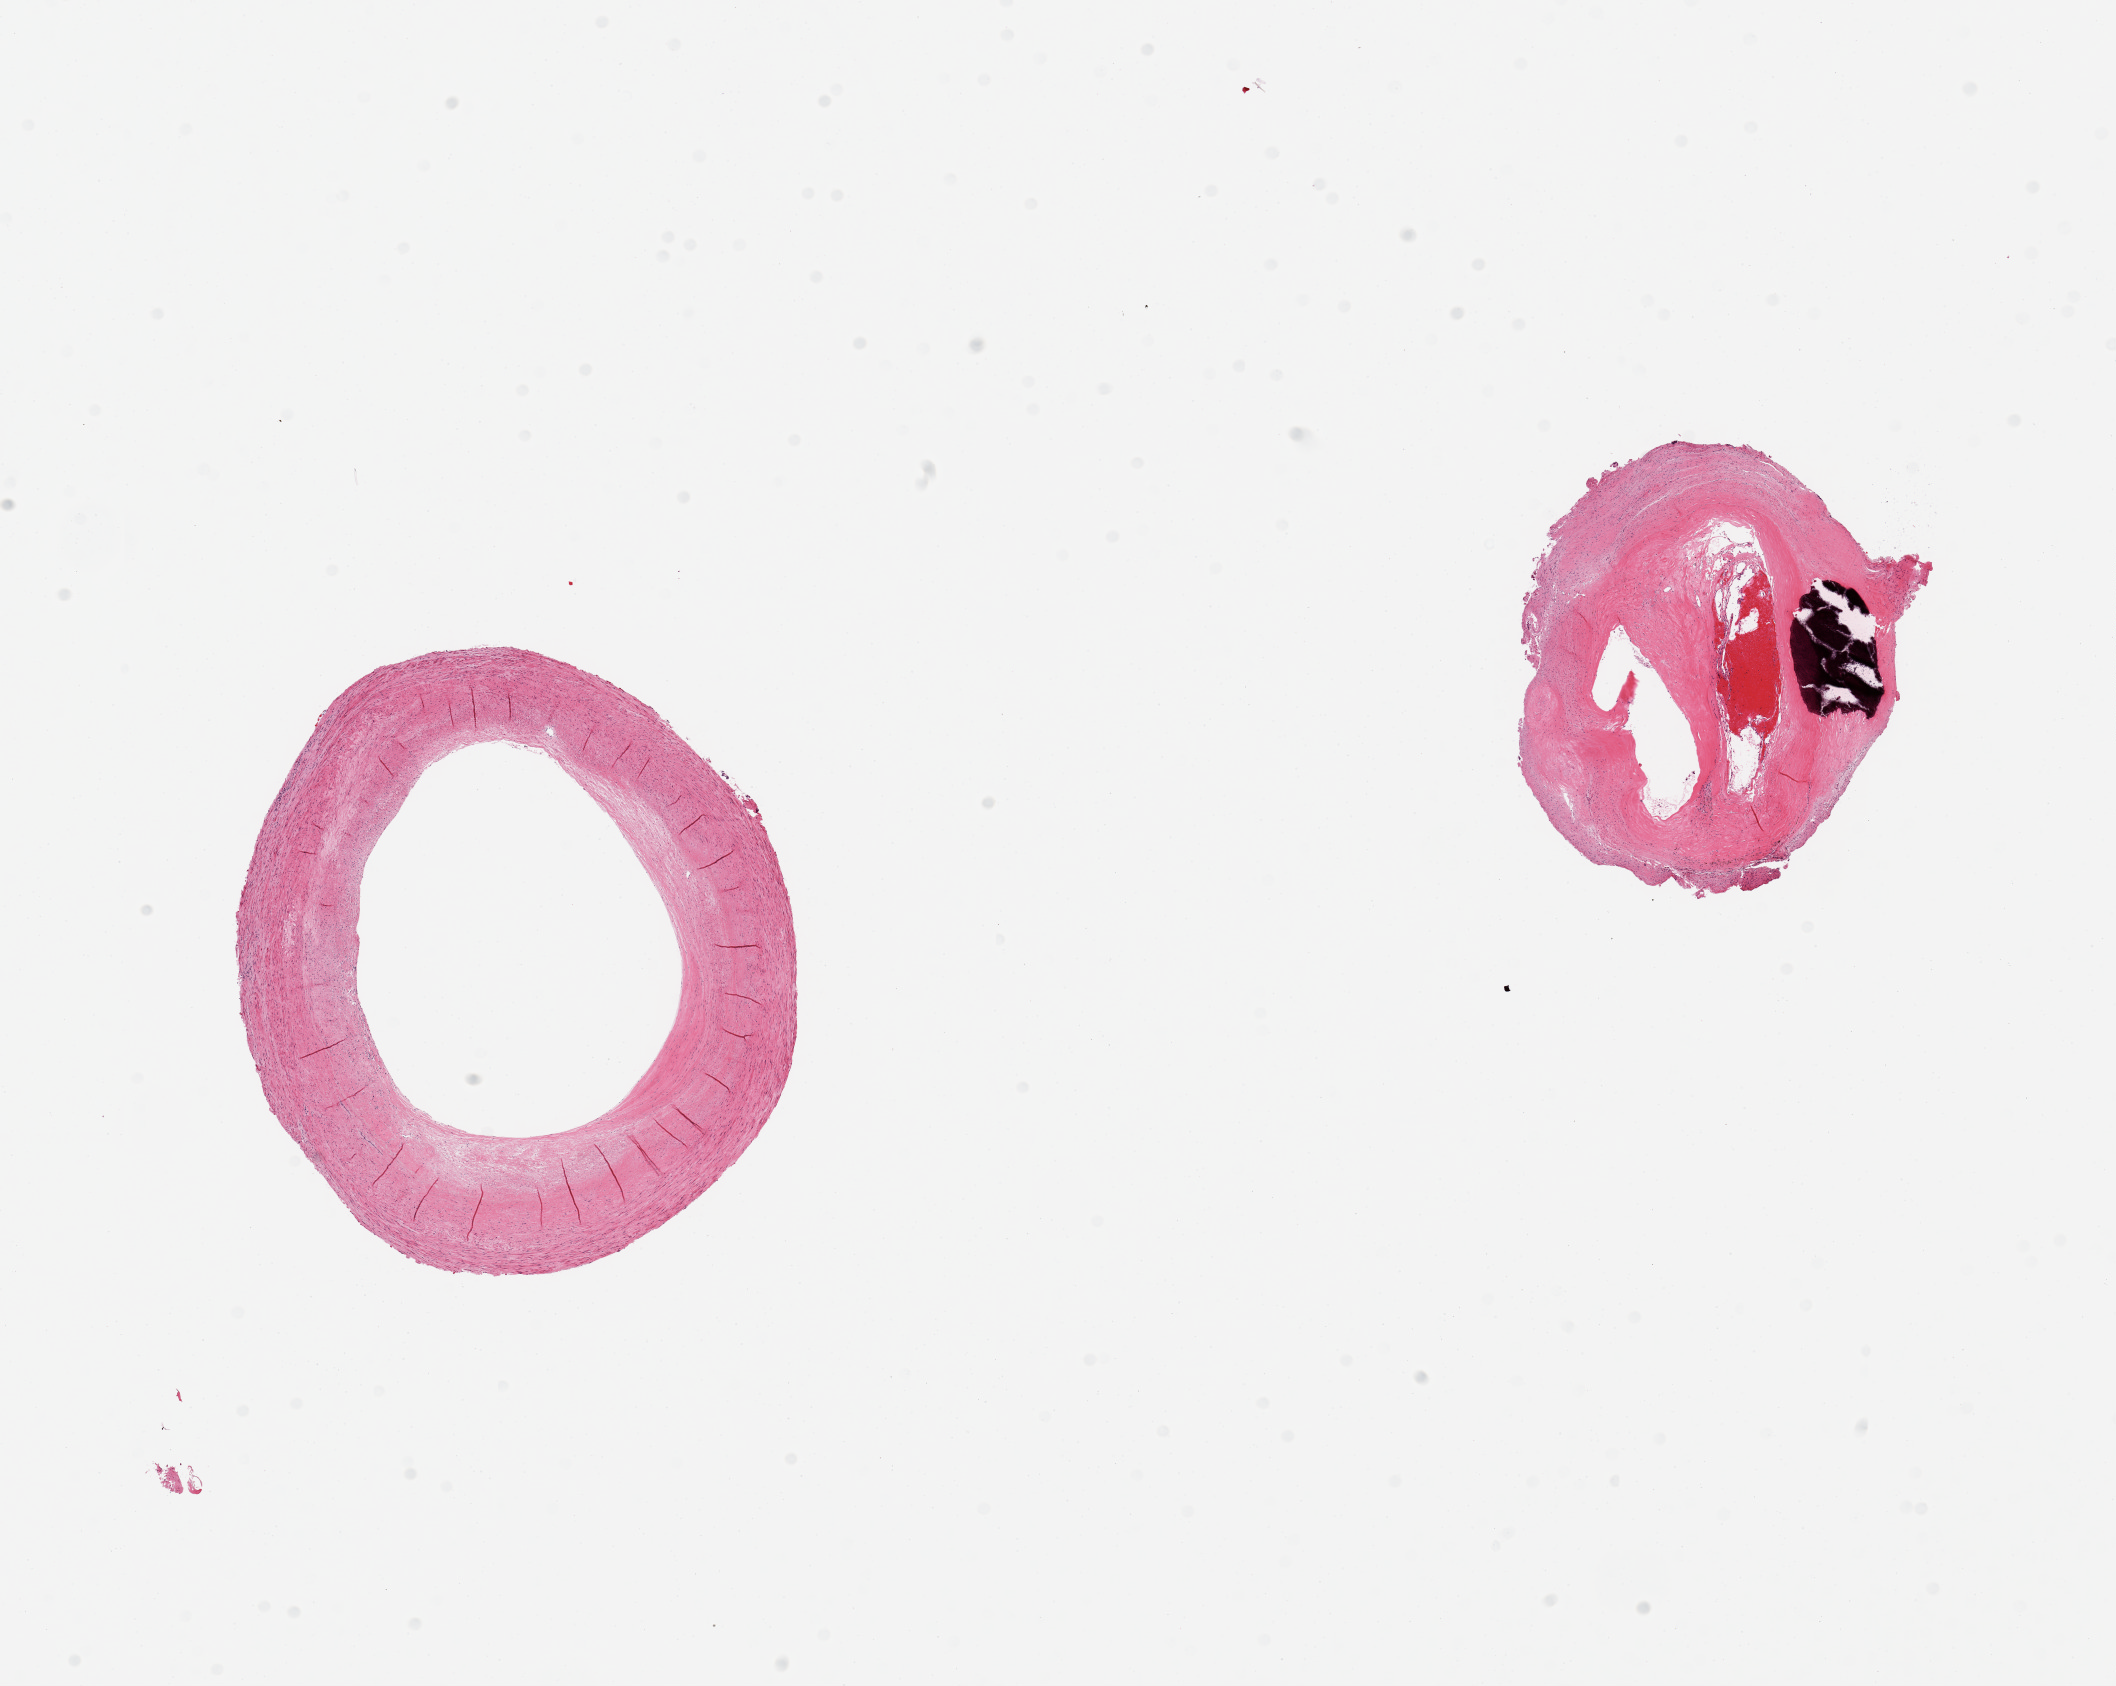
Digitized H&E-stained section, low-resolution overview of the scanned area, about 16.7 x 13.3 mm; PAXgene-fixed, paraffin-embedded tissue; target tissue: coronary artery; donor tissue sample. Male donor.
Review note (as recorded): 2 pieces, subtotally occlusive focally calcified atherosis.